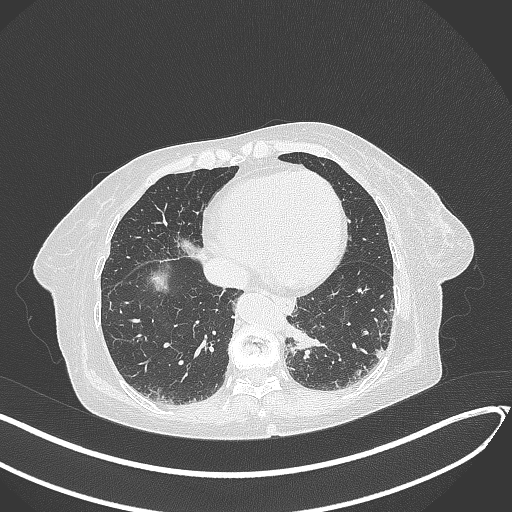
Chest CT, one axial slice; slice 60 of 324 in the series (ordered by position); reconstruction kernel B70f; lung window (W 1500 / L -600 HU); 1 mm slice thickness; 512 × 512 image matrix. Female patient, age 82 years. From the clinical record (not read from this slice): clinical TNM (as recorded): T1b N0 M1.
Annotated regions visible in this slice (bounding box drawn by a radiologist):
- lung tumour (recorded histology: adenocarcinoma): bounding box (x1, y1, x2, y2) in pixels: (287, 325, 326, 357)